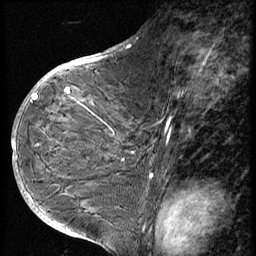
Breast MRI (dynamic contrast-enhanced), one sagittal slice; slice 32 of 56 in the series (ordered by position); 3 images stored at this slice position (order not interpretable as contrast timing); 1.5 T; TE 4.2 ms, TR 9 ms; 2.5 mm slice thickness; 256 × 256 image matrix, field of view 180 × 180 mm. Patient: female, 49 years. From the clinical record (not read from this slice): setting: breast cancer imaged before/during neoadjuvant chemotherapy; receptor status: HER2-positive.
Structures marked on this image (semi-automatic segmentation, software-assisted and operator-edited):
- analysis volume of interest (the breast-tissue region the enhancement analysis was run in; not a lesion): bounding box <37,85,131,207> (left, top, right, bottom; pixels)
- tumour enhancement mask (voxels above the 140 % enhancement threshold inside the analysis volume of interest): <37,88,70,98>